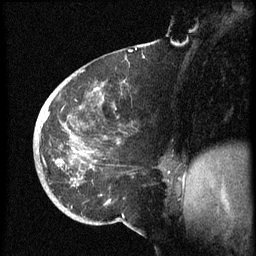
Breast MRI (dynamic contrast-enhanced), one sagittal slice. Position 24 of 60 along the scan axis. Dynamic contrast-enhanced series, image 2 of 3 at this slice position (ordered by acquisition). 1.5 T. TE 4.2 ms, TR 8.4 ms. 2.5 mm slice thickness. 256 × 256 image matrix, field of view 200 × 200 mm. Female patient, age 38 years. From the clinical record (not read from this slice): setting: breast cancer imaged before/during neoadjuvant chemotherapy; receptor status: HER2-positive.
Annotated regions visible in this slice (semi-automatic segmentation, software-assisted and operator-edited):
- analysis volume of interest (the breast-tissue region the enhancement analysis was run in; not a lesion): bounding box <34,74,173,202> (left, top, right, bottom; pixels)
- tumour enhancement mask (voxels above the 70 % enhancement threshold inside the analysis volume of interest): <37,88,99,181>